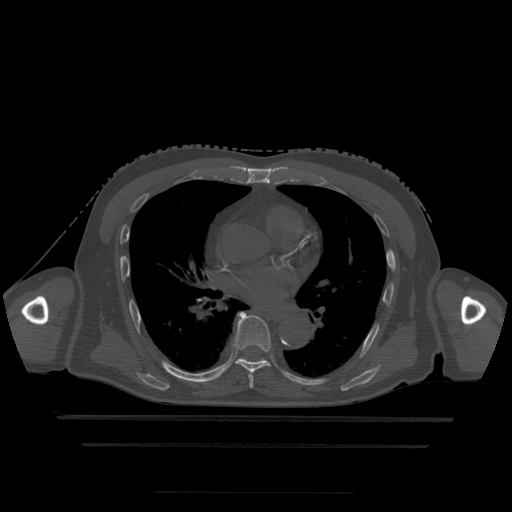
CT including the spine, one axial slice. Slice 298 of 522 in the series (ordered by position). Bone window (W 1800 / L 400 HU). 512 × 512 image matrix, field of view 436 × 436 mm. Patient age 68 years. Case-level facts recorded for this patient, not image findings: primary cancer: urothelial.
Annotated regions visible in this slice (semi-automatically segmented with operator editing):
- T6 vertebra: bounding box [x1, y1, x2, y2] px = [248, 375, 254, 389]
- T7 vertebra: [233, 312, 272, 374]
- T8 vertebra: [240, 357, 266, 362]